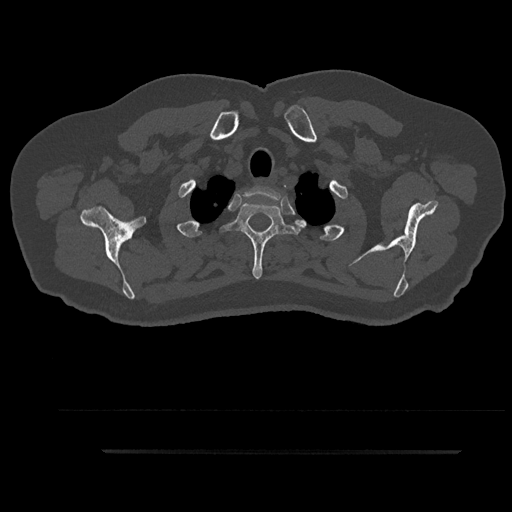
CT including the spine, one axial slice. Slice 762 of 797 in the series (ordered by position). 120 kVp. Bone window (W 1800 / L 400 HU). 512 × 512 image matrix, field of view 432 × 432 mm. Male patient, age 63 years. From the clinical record (not read from this slice): primary cancer: renal.
Outlined on this slice (semi-automatically segmented with operator editing):
- T1 vertebra: bounding box [x1, y1, x2, y2] px = [238, 186, 284, 217]
- T2 vertebra: [224, 202, 305, 279]